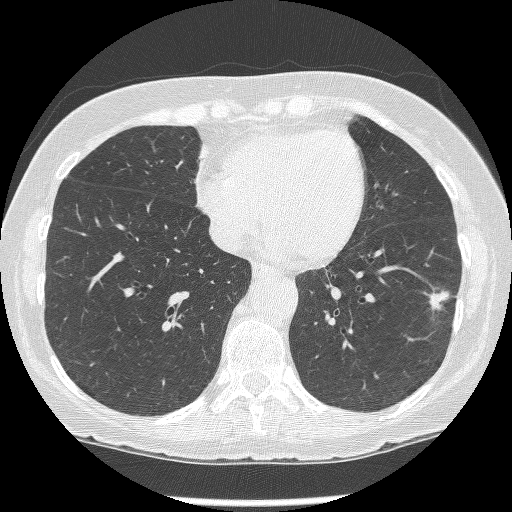
Axial slice from a low-dose chest CT screening exam; baseline annual screen; lung window (W 1500 / L -600 HU); 1.25 mm slice thickness; slice 86 of 247 in the series; 512 × 512 image matrix, field of view 303 × 303 mm. Female, age 62 years at enrolment. Former smoker at enrolment.
Lesion marked by an expert reader, bounding box [x1, y1, x2, y2] px = [421, 282, 462, 326]. The screening reader recorded 2 non-calcified nodules or masses ≥4 mm on this exam; which of them this box marks is not recorded. Participant outcome: lung cancer diagnosed 15 days after this screen — non-small cell carcinoma, left lower lobe, stage IIIB (AJCC 6th edition), 23 mm at pathology.